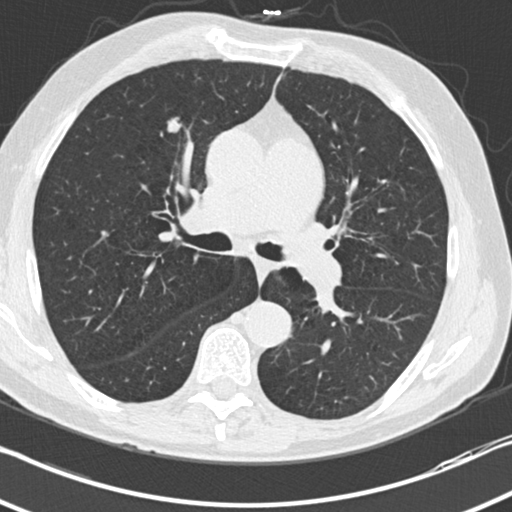
Low-dose screening chest CT, one axial slice; position 126 of 212 along the scan axis; lung window (W 1500 / L -600 HU); 512 × 512 image matrix, field of view 336 × 336 mm.
Outlined on this slice (outlined manually by an expert reader):
- lesion 1 (tumor, upper lobe of right lung): bounding box (x1, y1, x2, y2) in pixels: (168, 118, 181, 132)